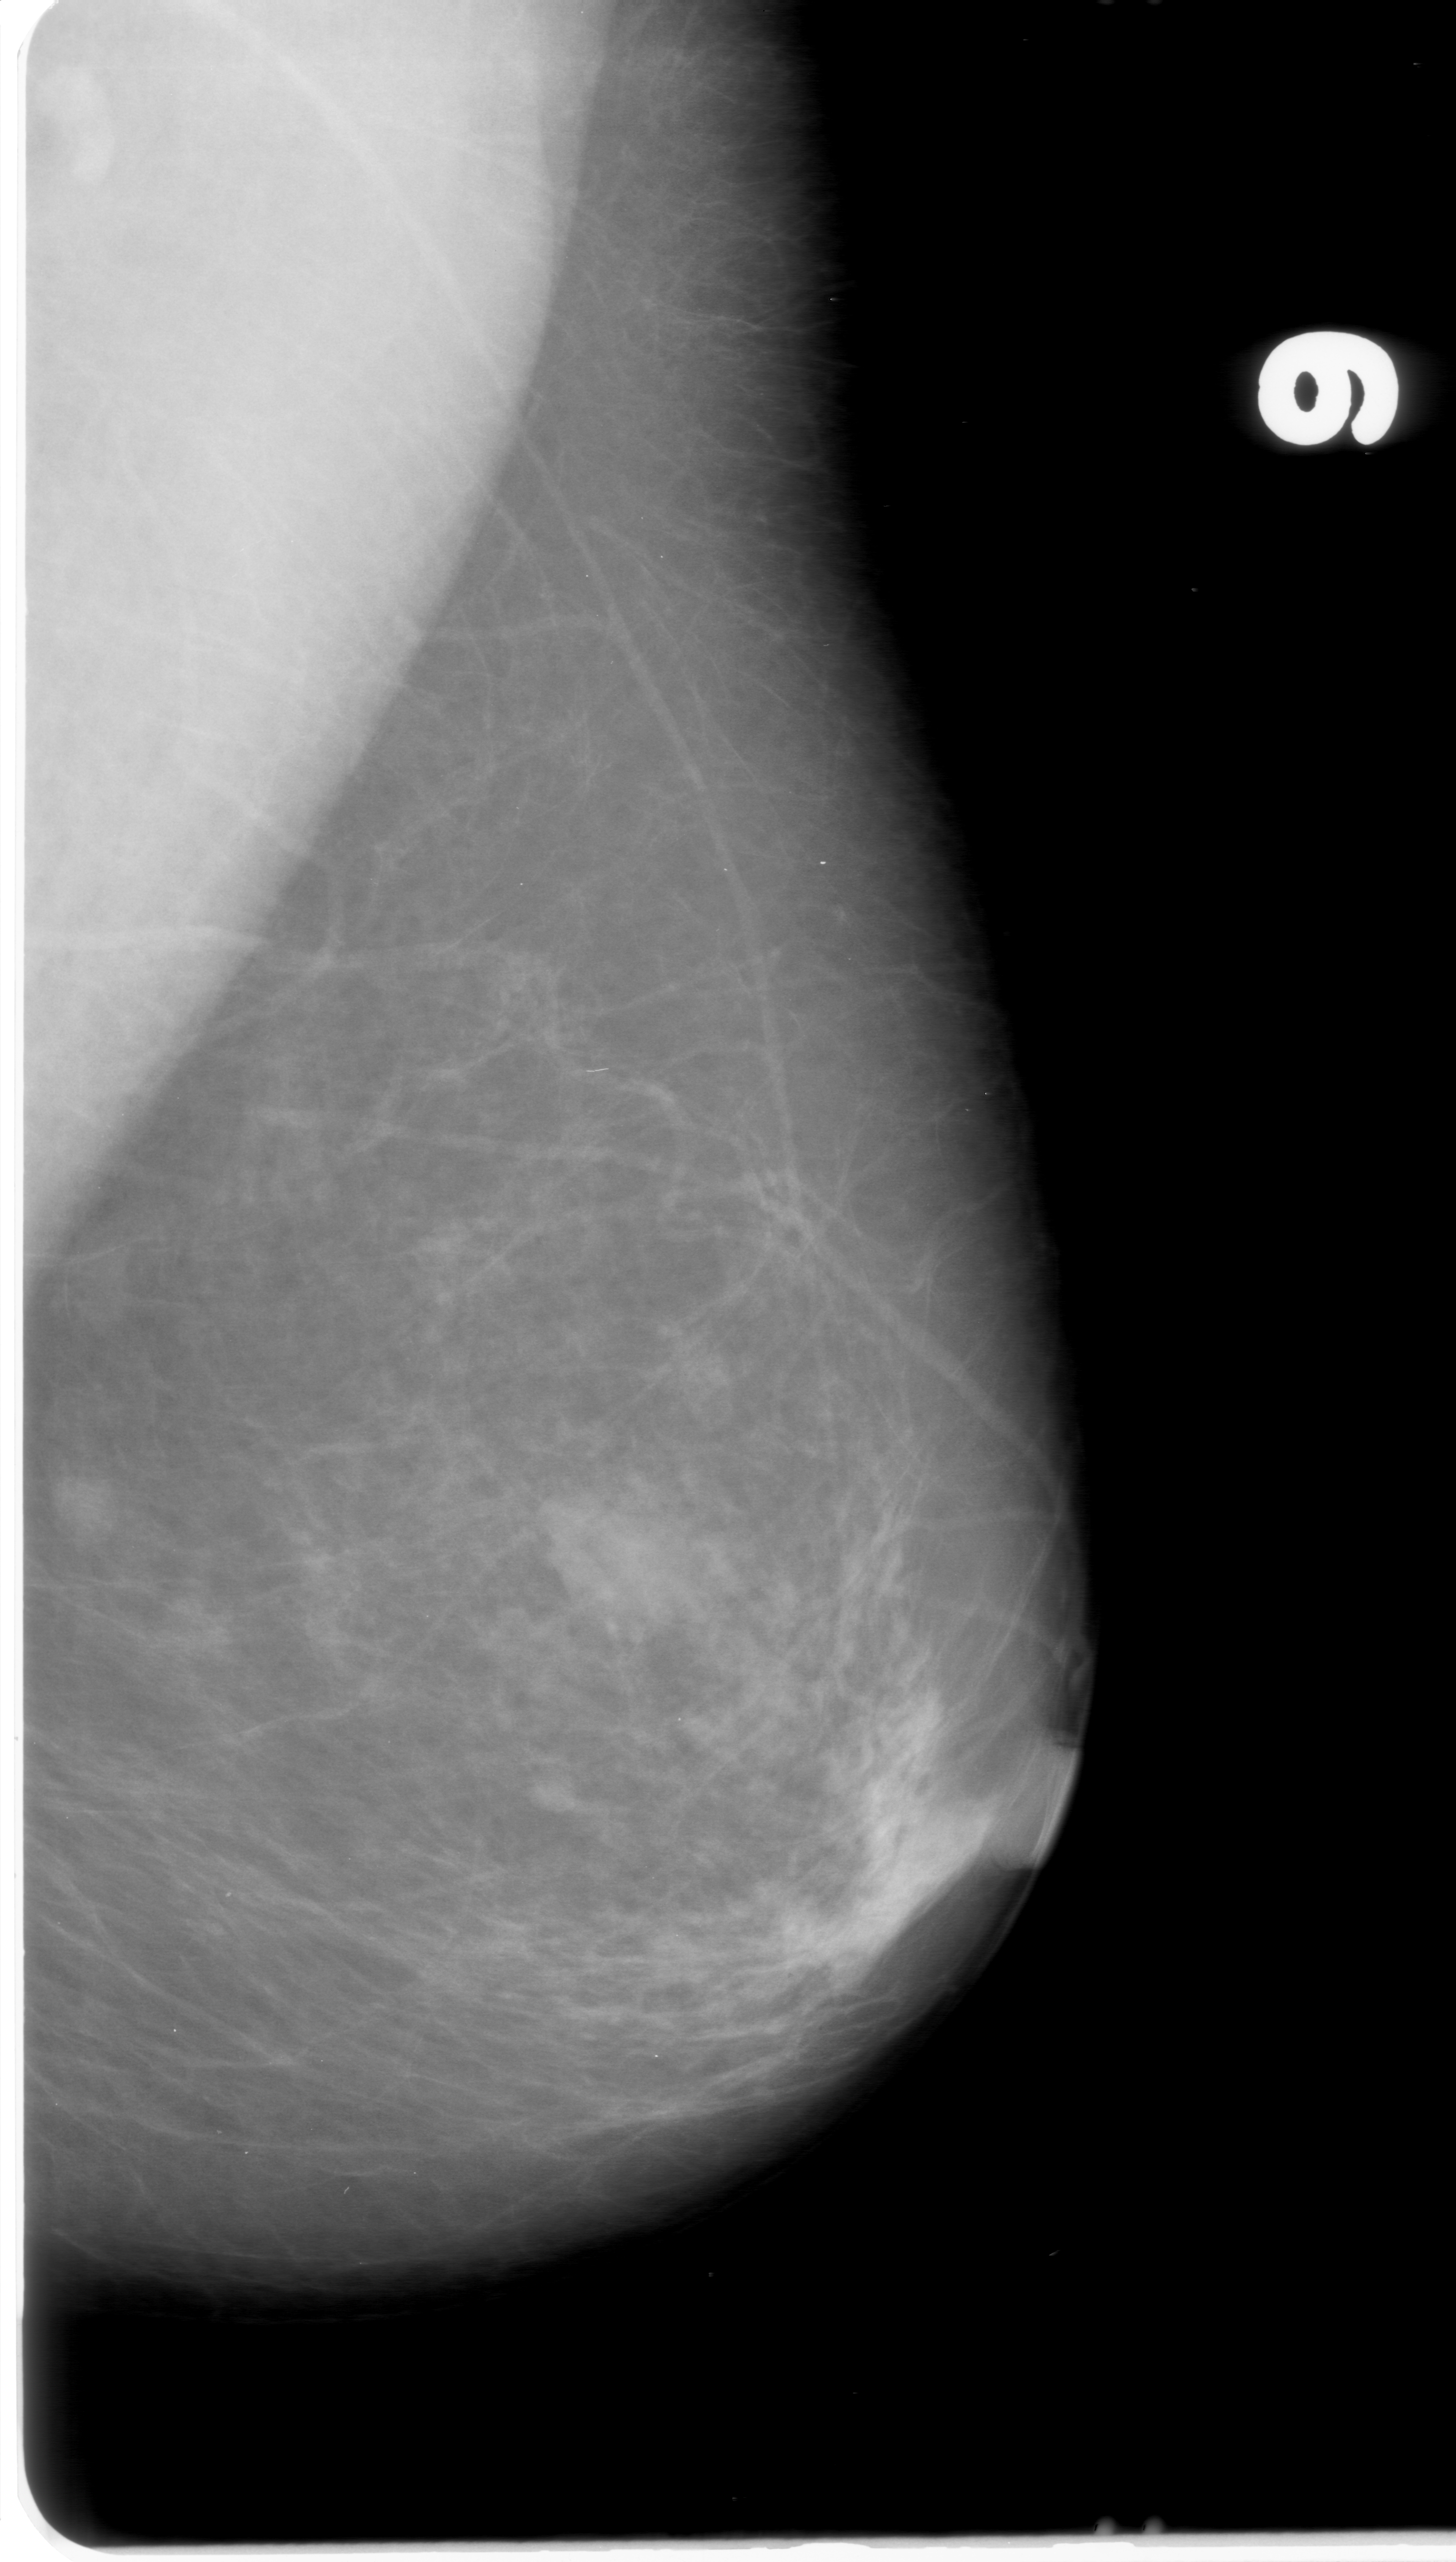
Mammogram (digitized film). Left breast. Mediolateral oblique (MLO) view. Breast composition: almost entirely fatty (BI-RADS density category 1 of 4). 1456 × 2562 image matrix.
Expert-marked regions of interest on this image (one box per marked abnormality):
- mass, shape oval, margins obscured; BI-RADS assessment category 0; pathology (as recorded): benign: bounding box <513,1484,686,1649> (left, top, right, bottom; pixels)